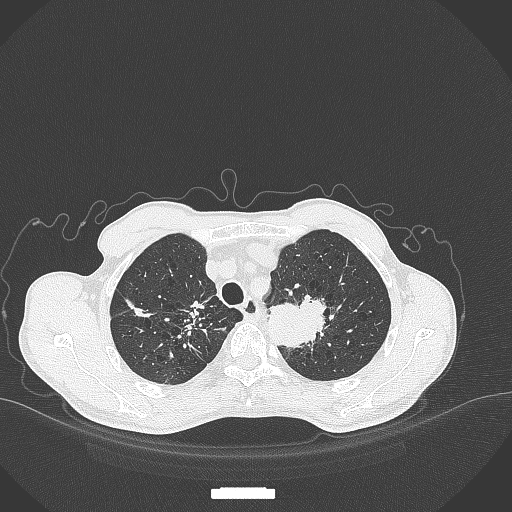
Chest CT, one axial slice; 120 kVp; lung window (W 1500 / L -600 HU); 512 × 512 image matrix, field of view 400 × 400 mm. Patient: male, 65 years. From the clinical record (not read from this slice): clinical TNM (as recorded): T2b N0 M0; histopathological grade: G2.
Structures marked on this image (rectangle marked by the reading radiologist):
- lung tumour (recorded histology: adenocarcinoma): box from (x=265, y=286) to (x=328, y=350) px